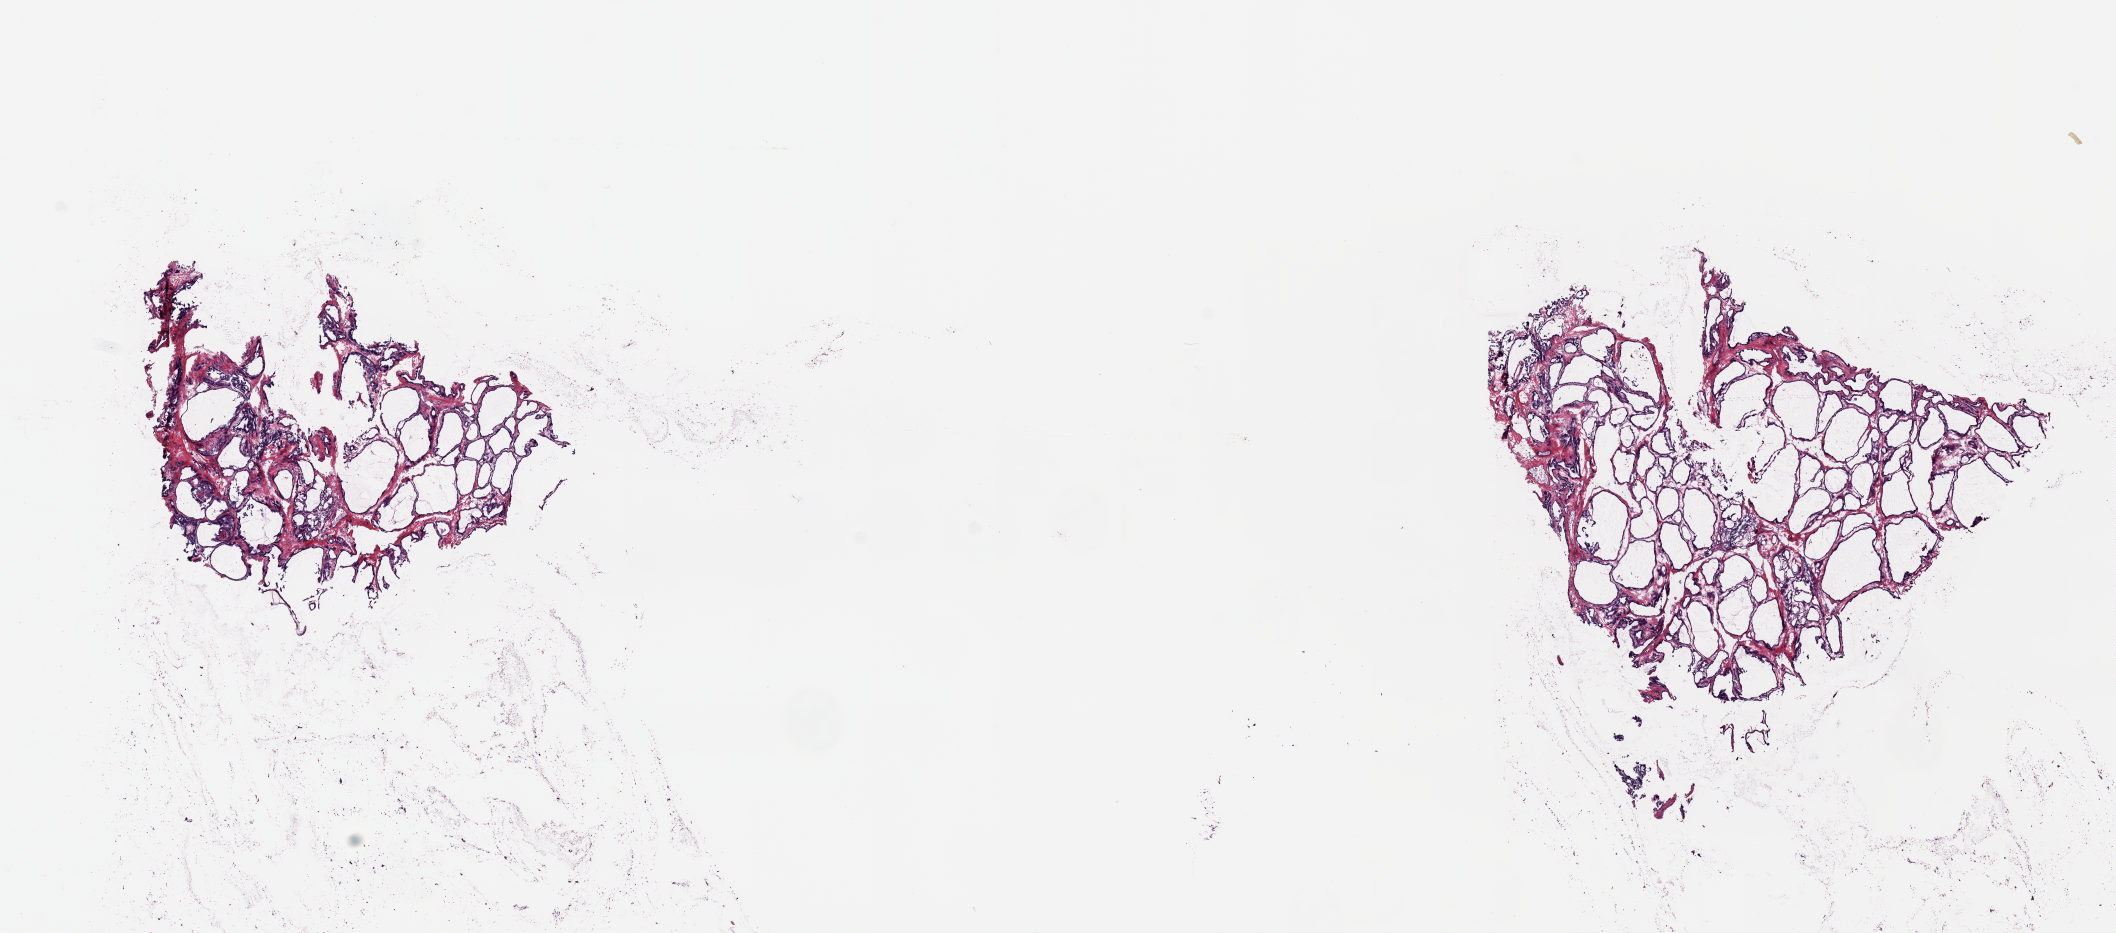
H&E whole-slide image — a low-resolution overview of the entire scanned area, about 16.7 x 7.4 mm. Frozen section. Thyroid, solid tissue normal (non-tumour tissue) sample. Male patient; age at initial diagnosis 19 years.
This section: solid tissue normal sample (biorepository sample class). Patient diagnosis: Papillary adenocarcinoma, NOS (thyroid gland).